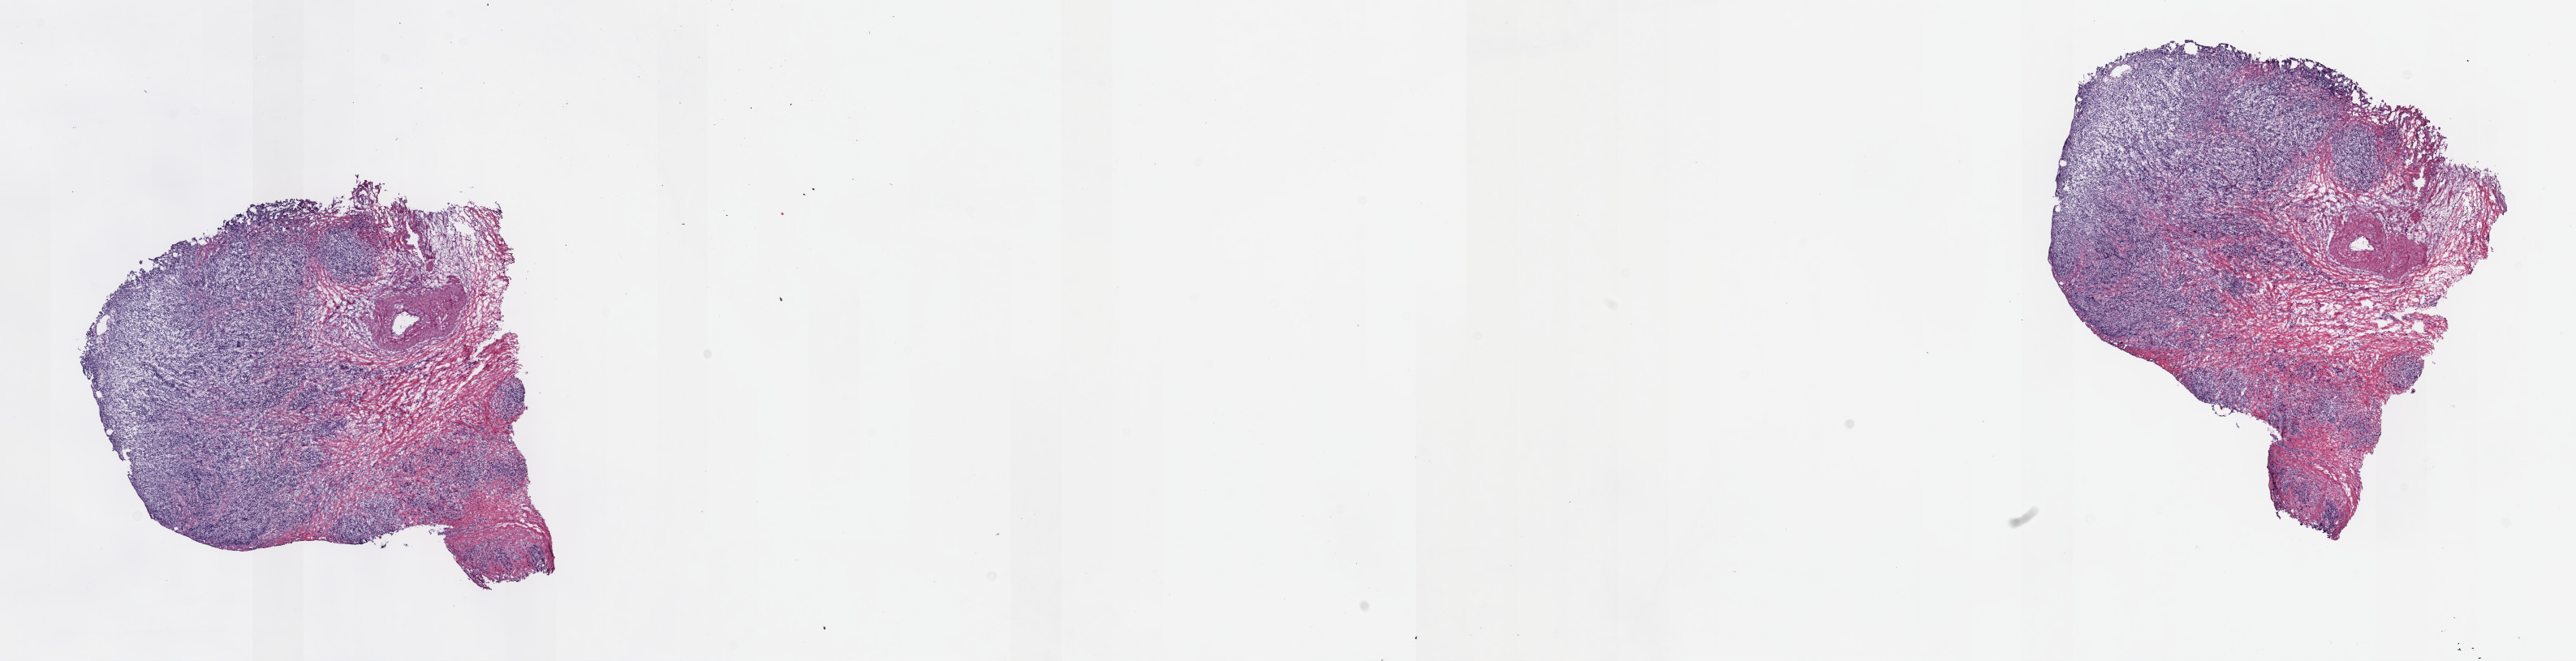
Whole-slide histology image, H&E-stained, low-resolution overview of the scanned area, about 25.7 x 6.6 mm, frozen section from the top of the tissue portion, stomach, primary tumour sample. Male patient. Histologic grade: G3 (poorly differentiated). Pathologist review of this section (percent, as recorded): tumour cells 70%, tumour nuclei 80%, normal cells 15%, stromal cells 15%, necrosis 0%. Inflammatory infiltration, as recorded: lymphocyte infiltration 0%, monocyte infiltration 0%, neutrophil infiltration 0%.
AJCC pathologic stage: IIIA (6th edition). Pathologic diagnosis: Tubular adenocarcinoma (body of stomach).